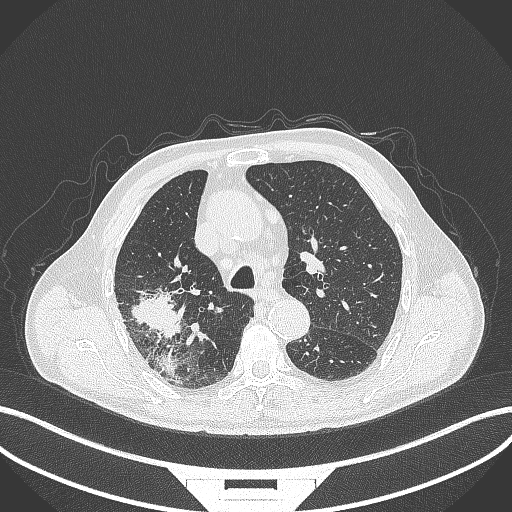
Chest CT, one axial slice. Slice 285 of 429 in the series (ordered by position). Reconstruction kernel B70f. Lung window (W 1500 / L -600 HU). 1 mm slice thickness. 512 × 512 image matrix, field of view 400 × 400 mm. Male patient, age 72 years. Case-level facts recorded for this patient, not image findings: clinical TNM (as recorded): T3 N2 M0.
Structures marked on this image (bounding box drawn by a radiologist):
- lung tumour (recorded histology: adenocarcinoma): box from (x=132, y=285) to (x=191, y=340) px